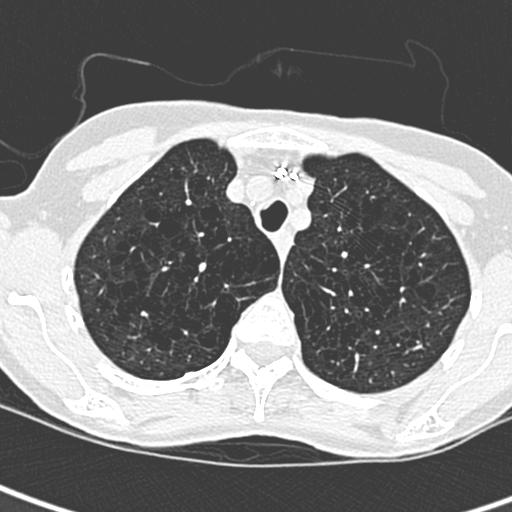
Axial slice from a low-dose chest CT screening exam, baseline annual screen, lung window (W 1500 / L -600 HU), 1.3 mm slice thickness, lung (sharp) reconstruction kernel (D), slice 54 of 259 in the series. Female participant, aged 71 years at enrolment.
Expert-annotated lung lesion, bounding box [x1, y1, x2, y2] px = [397, 328, 436, 365]. No non-calcified nodule or mass ≥4 mm was recorded by the screening reader at this exam. Official screen result: negative screen, no significant abnormalities.